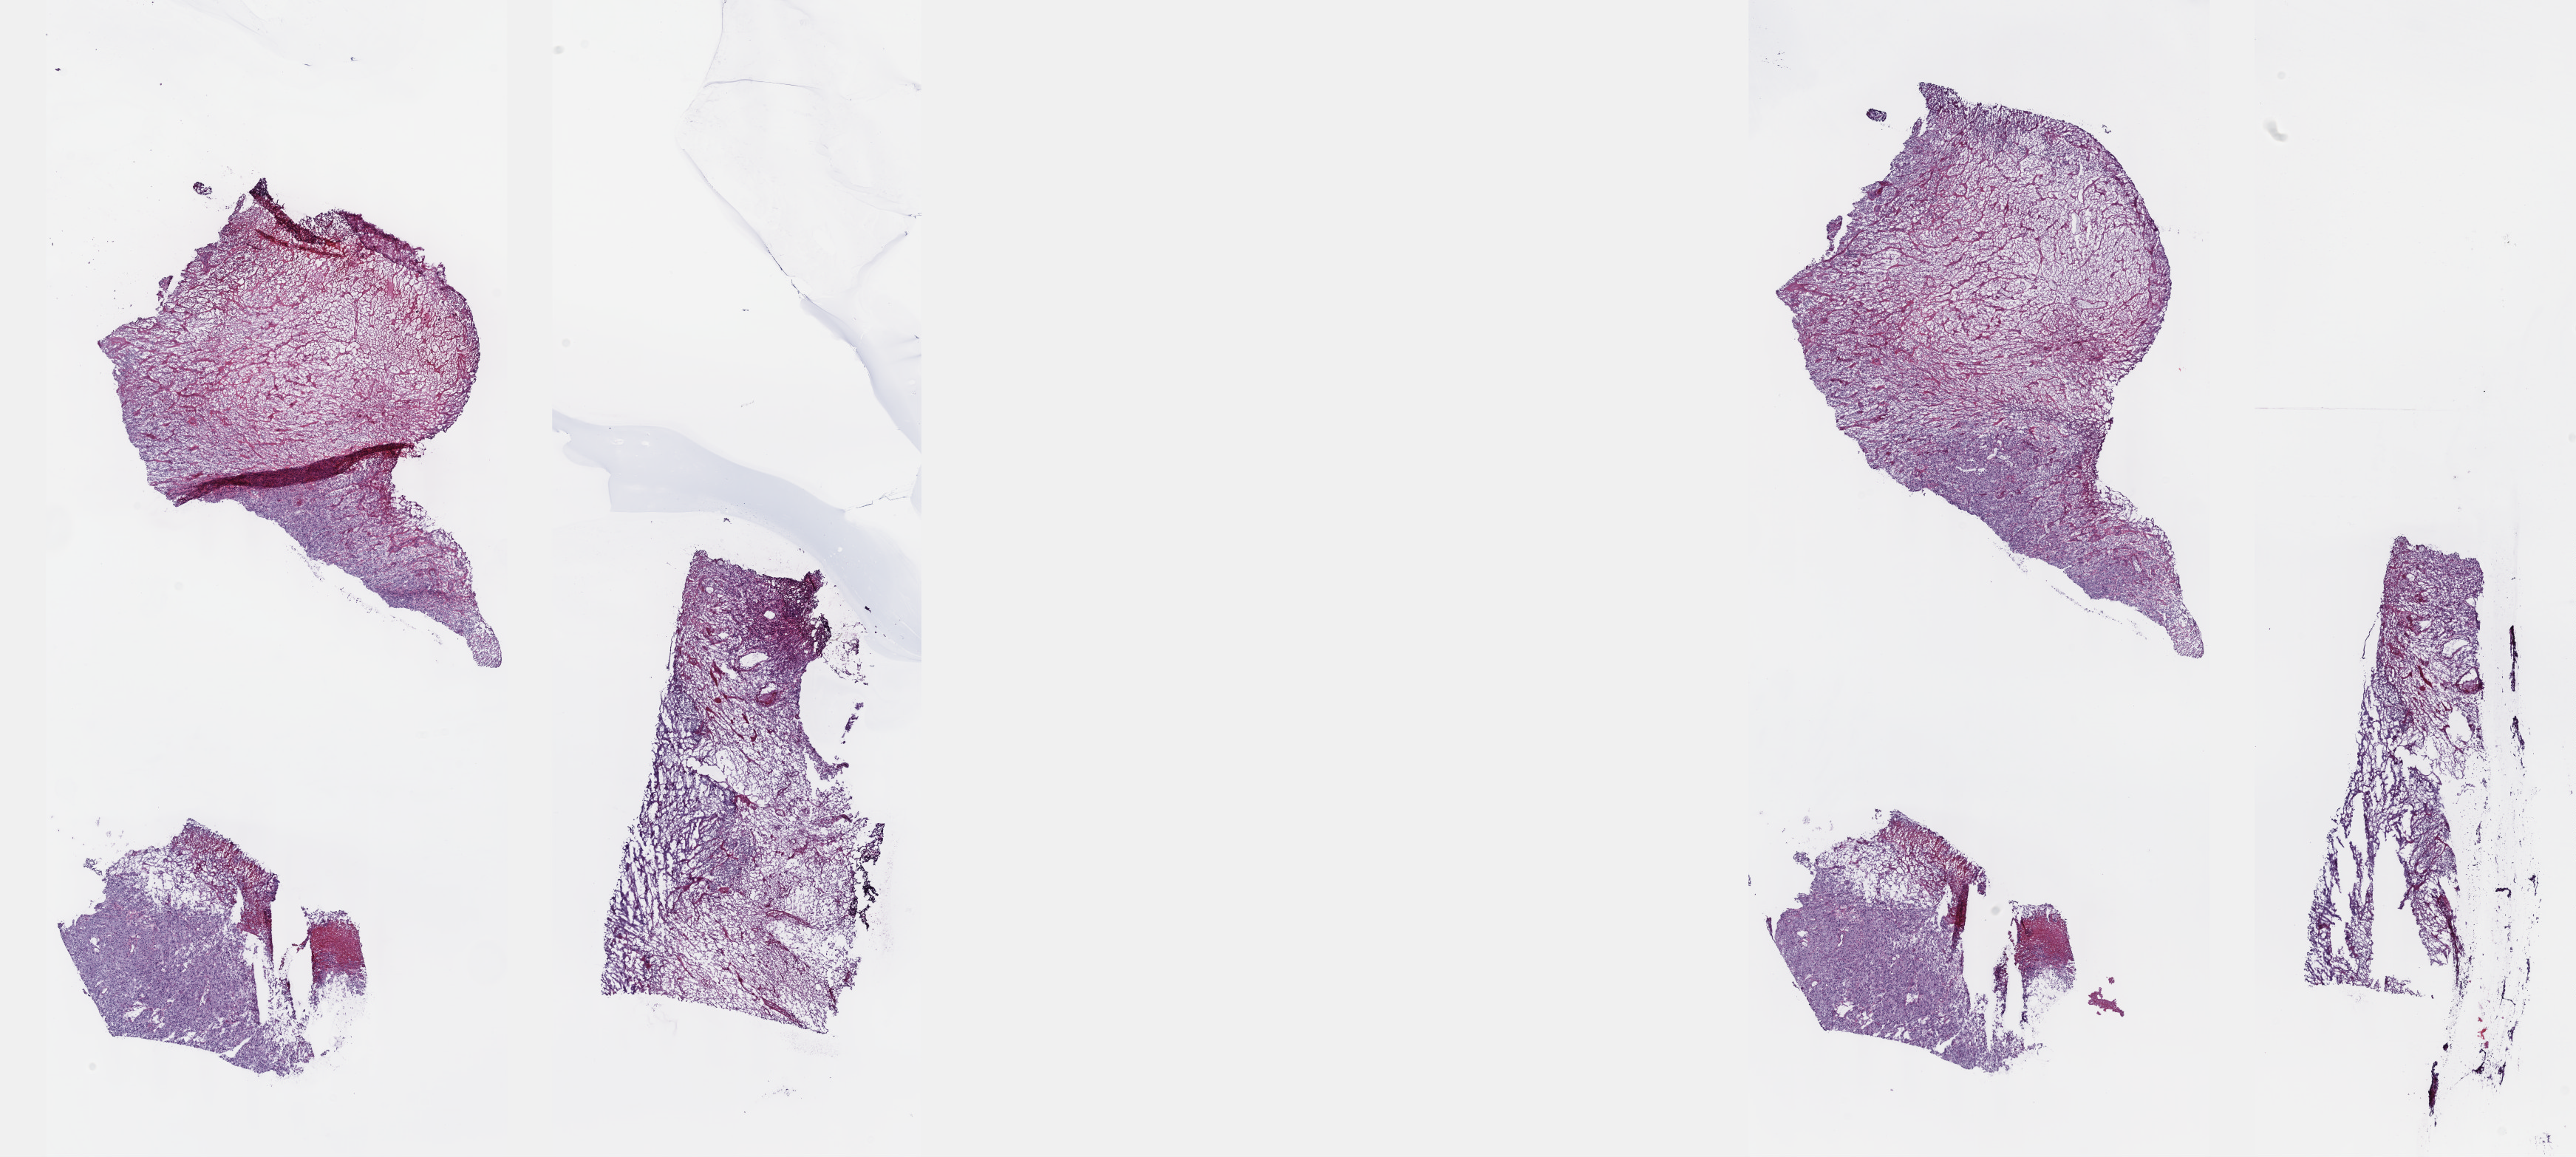
H&E-stained whole-slide image, whole scanned area (about 28.2 x 12.7 mm) shown as a low-resolution overview, frozen section from the top of the tissue portion, retroperitoneum and peritoneum, primary tumour sample. Female patient; age at initial diagnosis 70 years. Pathologist review of this section (percent, as recorded): tumour cells 100%, tumour nuclei 80%.
Diagnosis: Leiomyosarcoma, NOS (retroperitoneum).